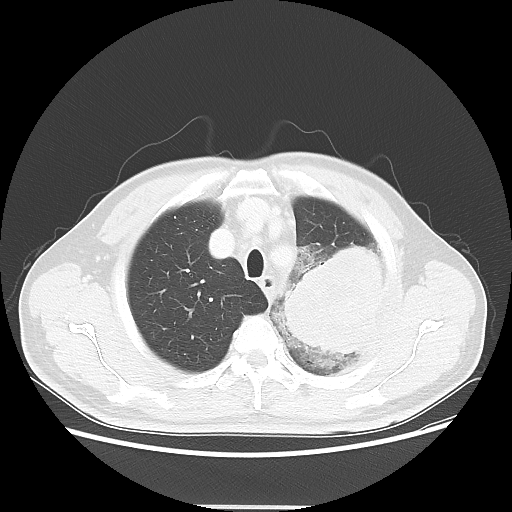
Chest CT, one axial slice; slice 45 of 53 in the series (ordered by position); reconstruction kernel LUNG; 100 kVp; lung window (W 1500 / L -600 HU); 5 mm slice thickness; 512 × 512 image matrix, field of view 391 × 391 mm. Patient: male, 60 years. Case-level facts recorded for this patient, not image findings: clinical TNM (as recorded): T4 N1 M1a; histopathological grade: G3.
Structures marked on this image (bounding box drawn by a radiologist):
- lung tumour (recorded histology: large cell carcinoma): box from (x=274, y=247) to (x=390, y=360) px